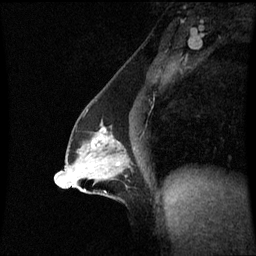
Breast MRI (dynamic contrast-enhanced), one sagittal slice; position 35 of 60 along the scan axis; dynamic contrast-enhanced series, image 2 of 3 at this slice position (ordered by acquisition); 1.5 T; TE 4.2 ms, TR 8.9 ms; 2.2 mm slice thickness; 256 × 256 image matrix, field of view 210 × 210 mm. Patient: female, 47 years. Case-level facts recorded for this patient, not image findings: setting: breast cancer imaged before/during neoadjuvant chemotherapy; receptor status: HR-positive, HER2-negative.
Outlined on this slice (semi-automatically segmented with operator editing):
- analysis volume of interest (the breast-tissue region the enhancement analysis was run in; not a lesion): bounding box (x1, y1, x2, y2) in pixels: (64, 121, 134, 196)
- tumour enhancement mask (voxels above the 70 % enhancement threshold inside the analysis volume of interest): (94, 138, 120, 166)